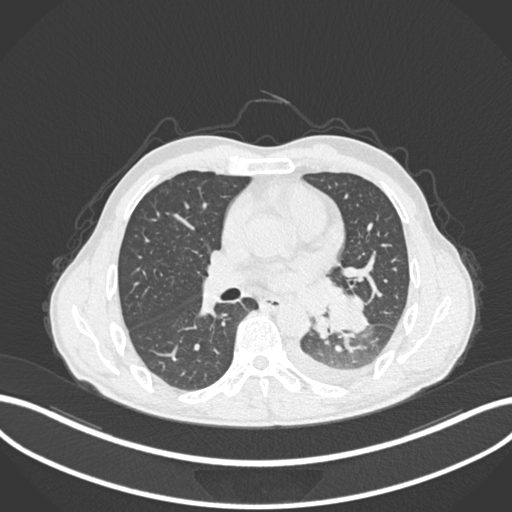
Chest CT, one axial slice; position 127 of 222 along the scan axis; reconstruction kernel B30f; 120 kVp; lung window (W 1500 / L -600 HU); 1 mm slice thickness; 512 × 512 image matrix. Patient: male, 47 years. Case-level facts recorded for this patient, not image findings: clinical TNM (as recorded): T3 N1 M1c; histopathological grade: G3.
Structures marked on this image (rectangle marked by the reading radiologist):
- lung tumour (recorded histology: small cell carcinoma): bounding box <323,287,375,337> (left, top, right, bottom; pixels)